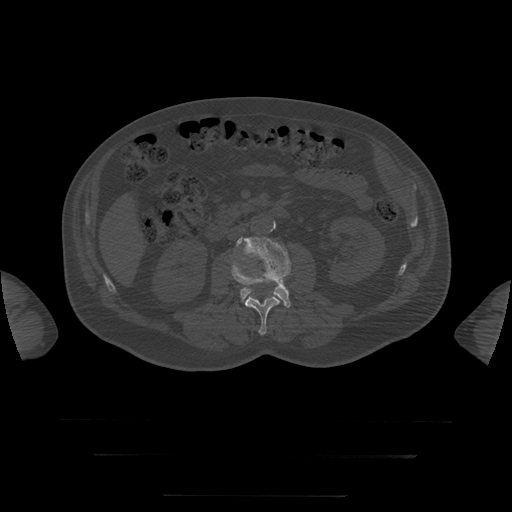
CT including the spine, one axial slice. Position 12 of 397 along the scan axis. Reconstruction kernel STANDARD. Bone window (W 1800 / L 400 HU). 1.25 mm slice thickness. 512 × 512 image matrix. Patient age 73 years. Case-level facts recorded for this patient, not image findings: primary cancer: prostate.
Annotated regions visible in this slice (semi-automatically segmented with operator editing):
- L3 vertebra: box from (x=236, y=237) to (x=292, y=308) px